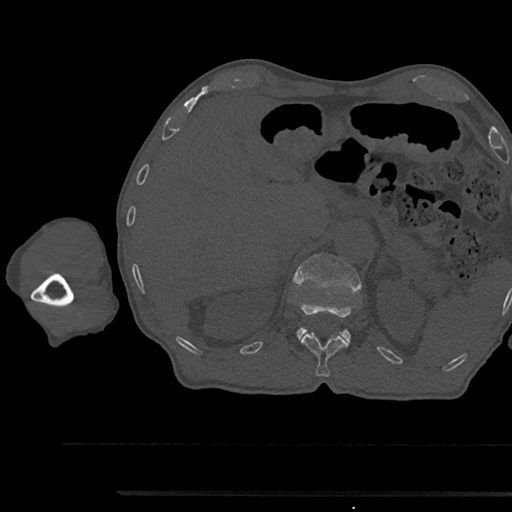
CT including the spine, one axial slice; slice 683 of 797 in the series (ordered by position); reconstruction kernel Br40s/3; 120 kVp; bone window (W 1800 / L 400 HU); 0.5 mm slice thickness; 512 × 512 image matrix, field of view 367 × 367 mm. Male patient, age 79 years. From the clinical record (not read from this slice): primary cancer: prostate.
Outlined on this slice (semi-automatic segmentation, software-assisted and operator-edited):
- L1 vertebra: box from (x=293, y=254) to (x=361, y=342) px
- T12 vertebra: (x=301, y=333)–(x=349, y=377)